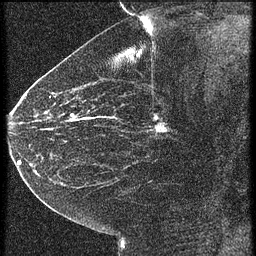
Breast MRI (dynamic contrast-enhanced), one sagittal slice. Position 33 of 60 along the scan axis. 4 images stored at this slice position (order not interpretable as contrast timing). 1.5 T. TE 4.2 ms, TR 21.3 ms. 256 × 256 image matrix. Female patient, age 43 years. From the clinical record (not read from this slice): setting: breast cancer imaged before/during neoadjuvant chemotherapy; receptor status: HER2-positive.
Annotated regions visible in this slice (semi-automatic segmentation, software-assisted and operator-edited):
- analysis volume of interest (the breast-tissue region the enhancement analysis was run in; not a lesion): bounding box [x1, y1, x2, y2] px = [122, 100, 187, 151]
- tumour enhancement mask (voxels above the 90 % enhancement threshold inside the analysis volume of interest): [154, 116, 167, 133]